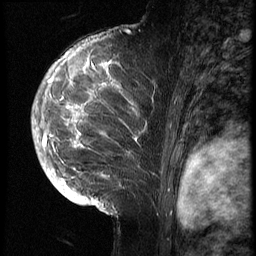
Breast MRI (dynamic contrast-enhanced), one sagittal slice. Position 43 of 70 along the scan axis. 3 images stored at this slice position (order not interpretable as contrast timing). 1.5 T. TE 4.2 ms, TR 9 ms. 2.5 mm slice thickness. 256 × 256 image matrix, field of view 180 × 180 mm. Patient: female, 28 years. From the clinical record (not read from this slice): setting: breast cancer imaged before/during neoadjuvant chemotherapy.
Annotated regions visible in this slice (semi-automatic segmentation, software-assisted and operator-edited):
- analysis volume of interest (the breast-tissue region the enhancement analysis was run in; not a lesion): bounding box <43,42,159,215> (left, top, right, bottom; pixels)
- tumour enhancement mask (voxels above the 140 % enhancement threshold inside the analysis volume of interest): <44,56,138,204>